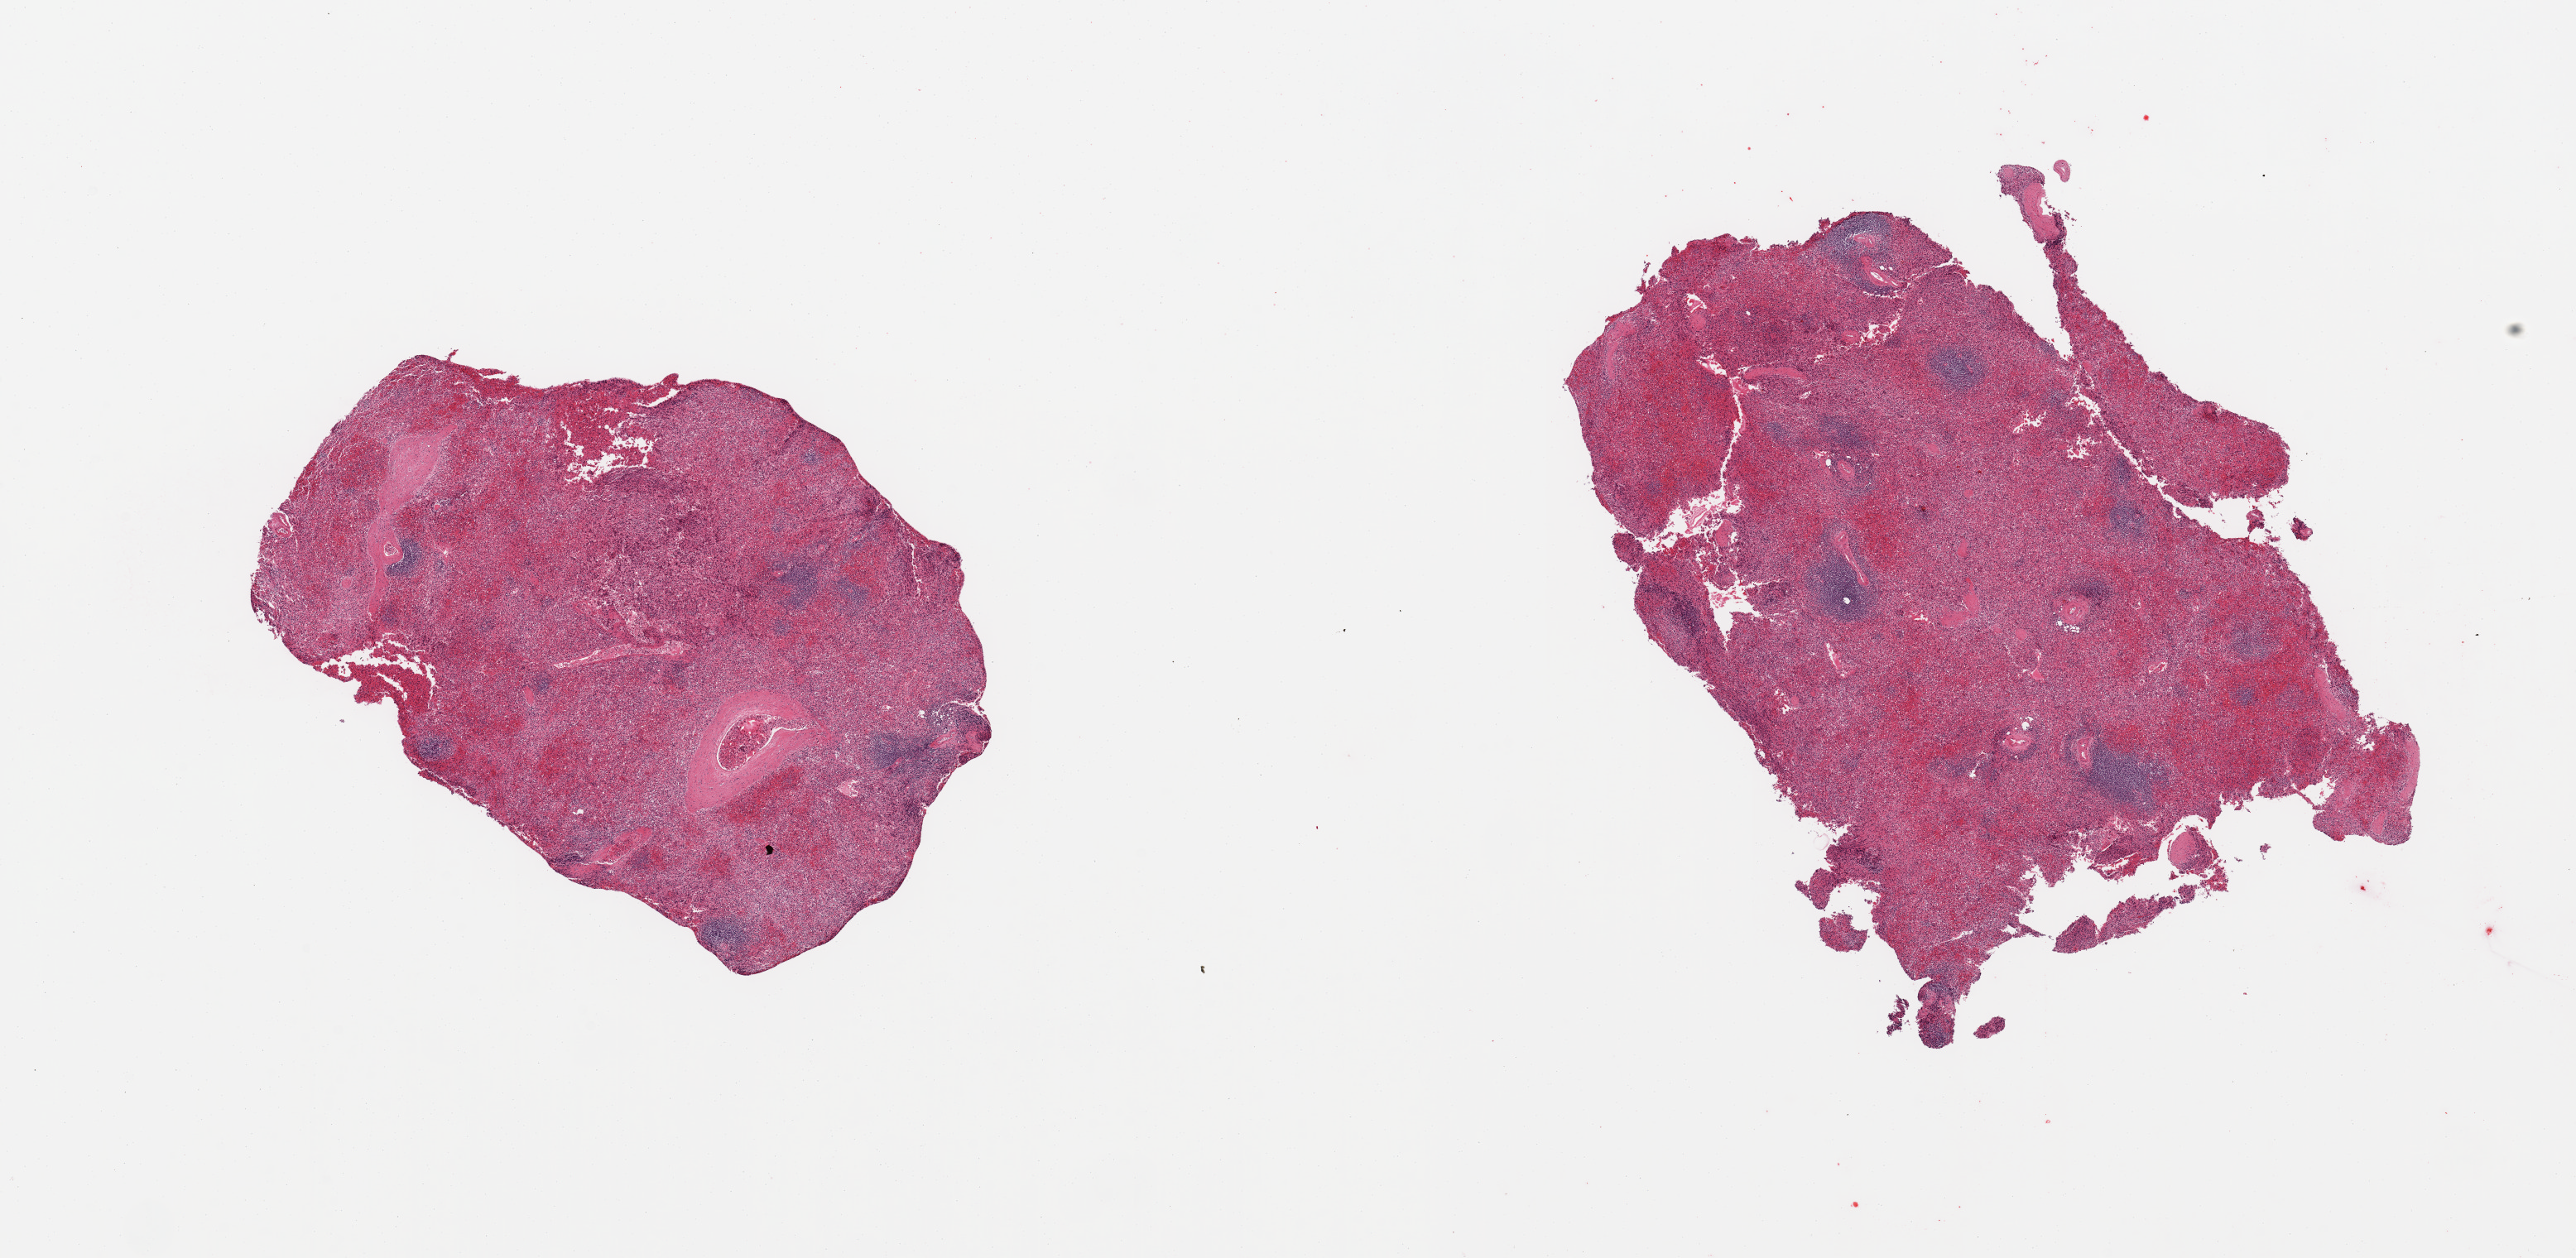
Whole-slide image, H&E stain, brightfield, low-resolution overview of the scanned area, about 24.6 x 12.0 mm, PAXgene-fixed paraffin-embedded (PFPE) section, target tissue: spleen, tissue donor sample. Donor: male.
Reviewer comment on this tissue sample: 2 pieces; patchy congestion.